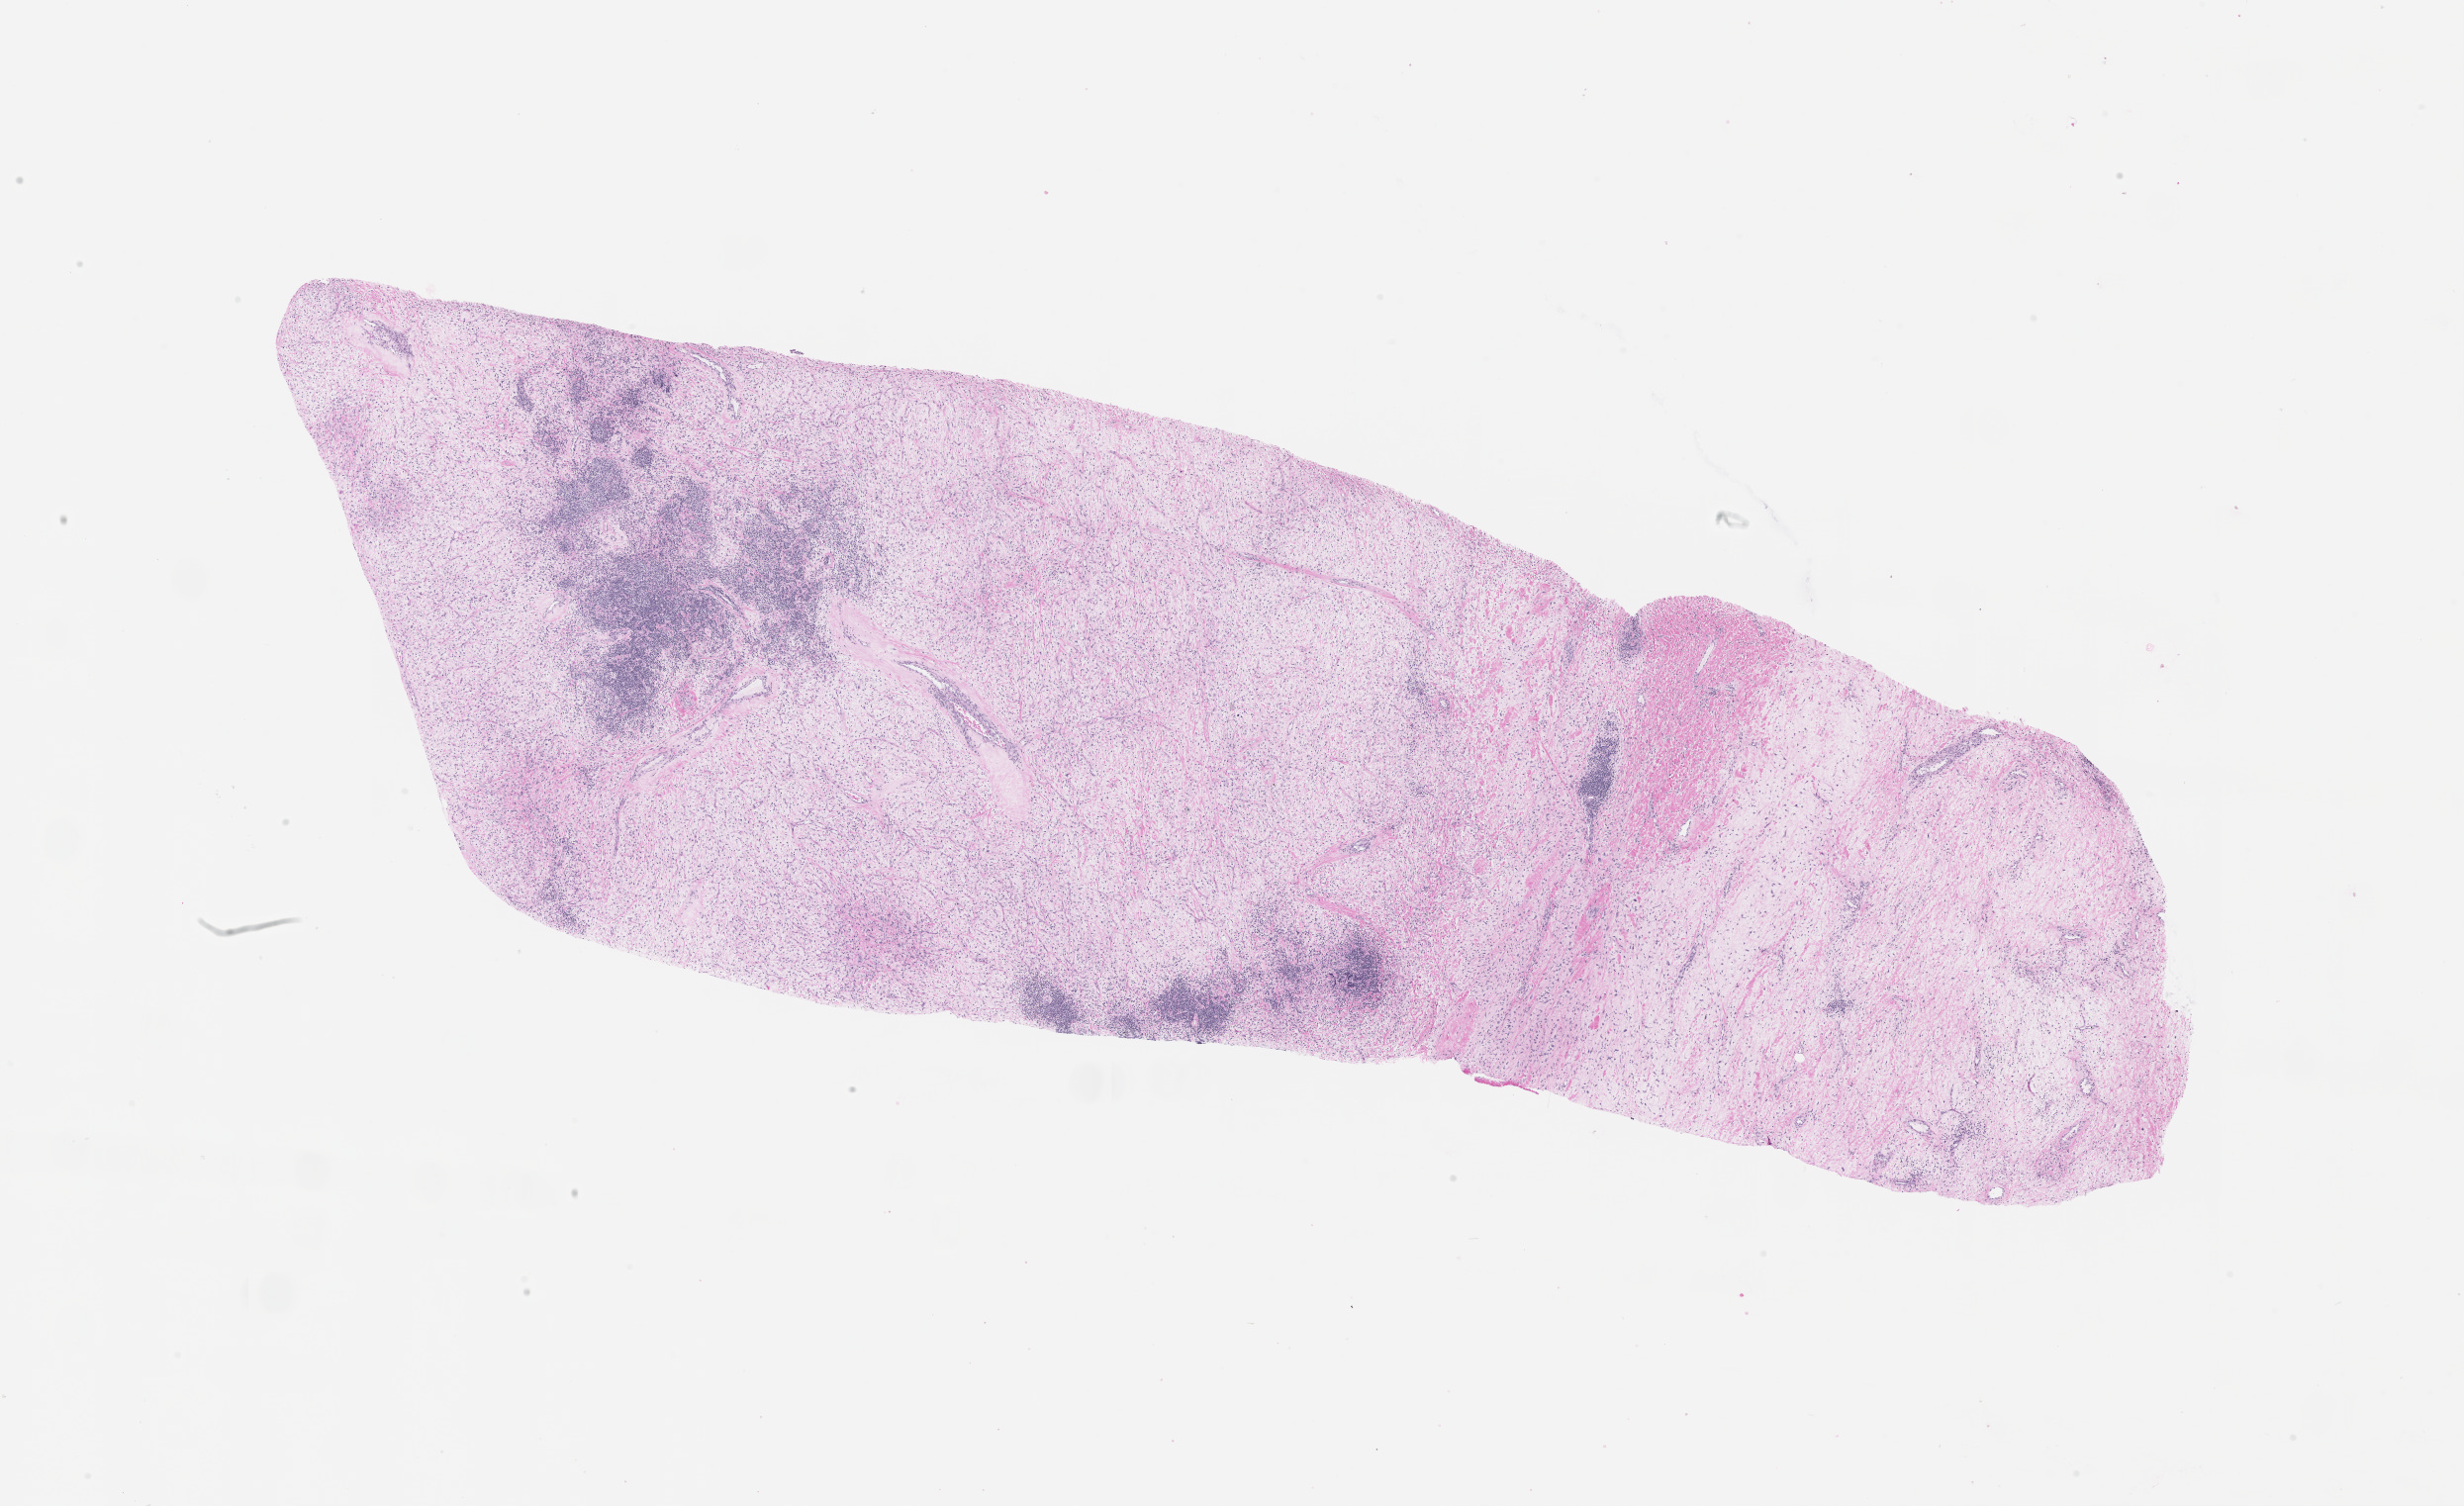
Digitized H&E tissue section (whole slide), whole scanned area (about 20.0 x 12.3 mm) shown as a low-resolution overview.
• patient diagnosis (cohort enrolment): sarcoma (site not recorded at cohort level)